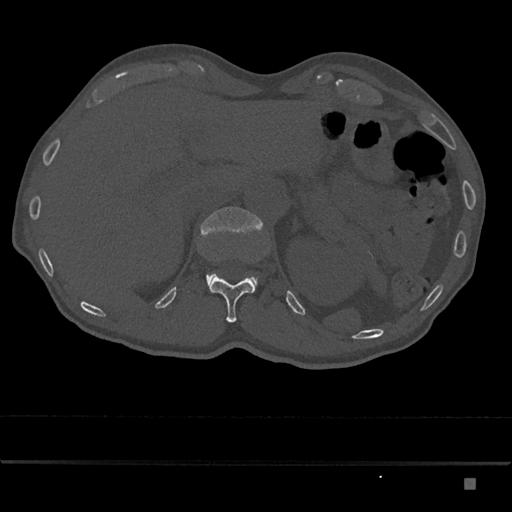
CT including the spine, one axial slice. Slice 591 of 797 in the series (ordered by position). 120 kVp. Bone window (W 1800 / L 400 HU). 512 × 512 image matrix, field of view 390 × 390 mm. Male patient, age 72 years. From the clinical record (not read from this slice): primary cancer: prostate.
Annotated regions visible in this slice (semi-automatic segmentation, software-assisted and operator-edited):
- L1 vertebra: bounding box <200,207,263,289> (left, top, right, bottom; pixels)
- T12 vertebra: <209,276,255,323>